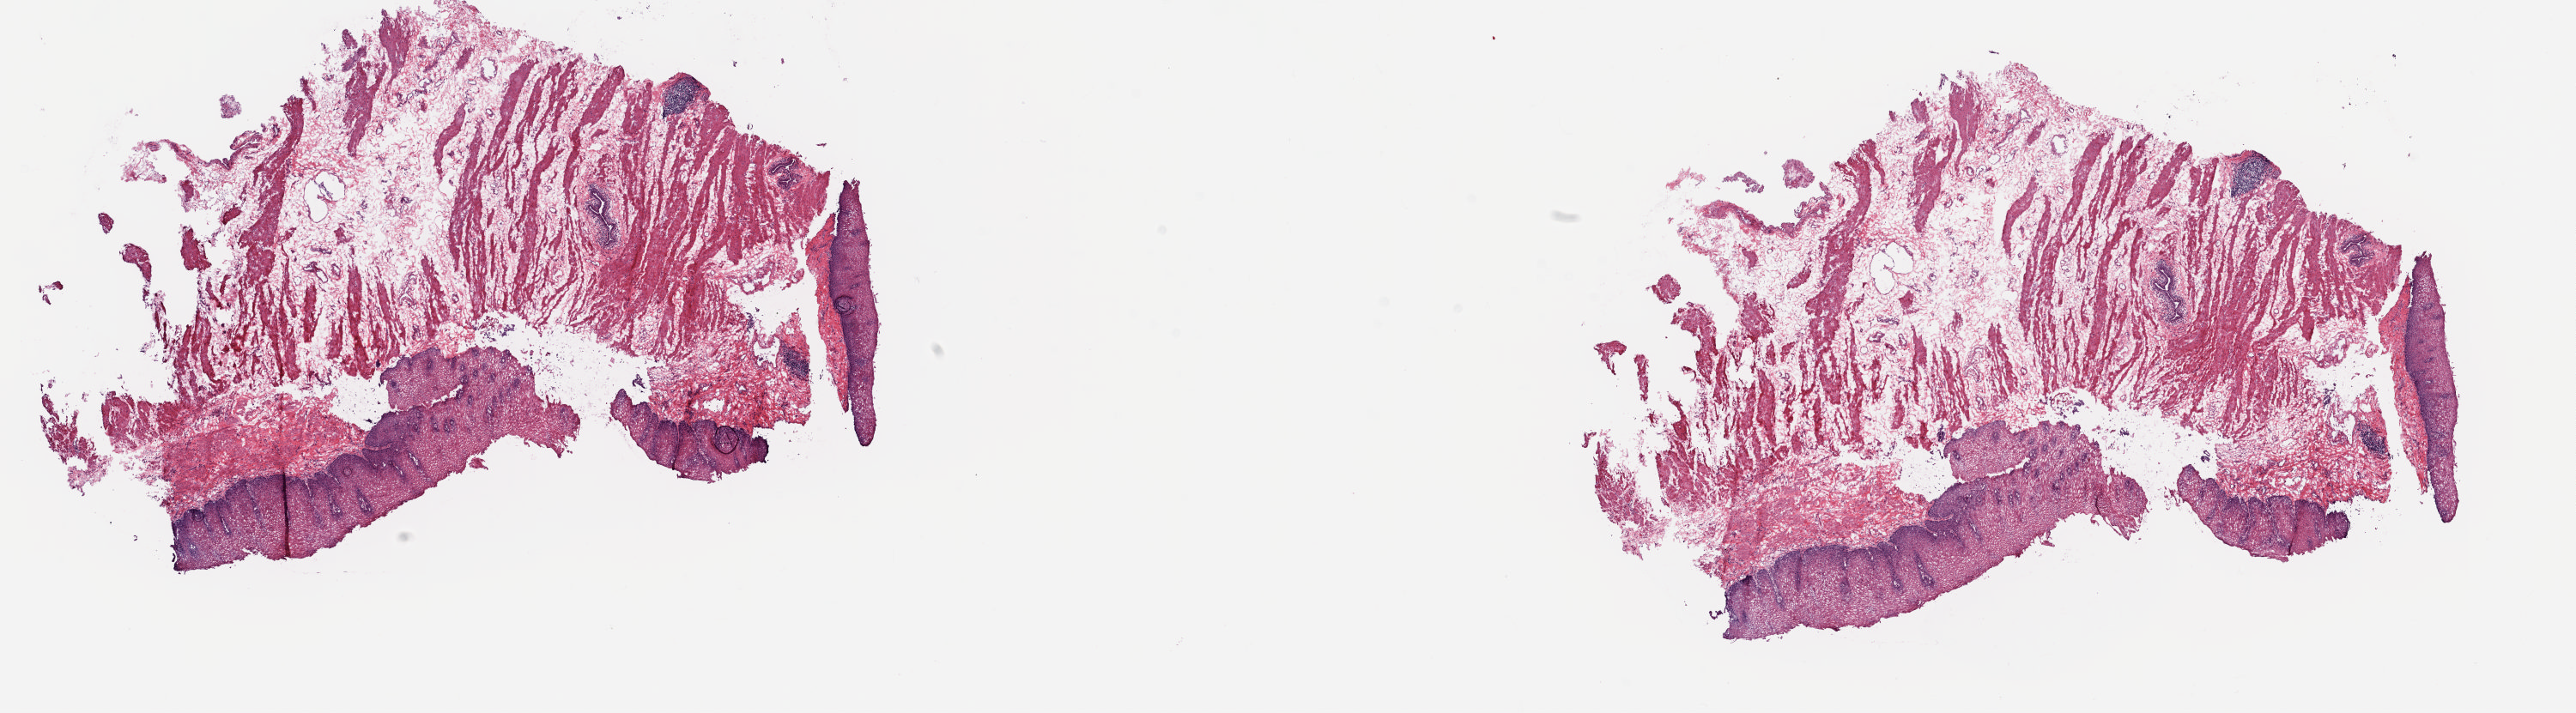
Digitized Hematoxylin and eosin (H&E) stained tissue section (whole slide), low-resolution overview of the scanned area, about 23.8 x 6.6 mm. Frozen section. Sample: solid tissue normal (non-tumour tissue), esophagus. Patient: male, age at initial diagnosis 59 years. Slide review estimates, as recorded: tumour cells 0%, tumour nuclei 0%, normal cells 15%, stromal cells 85%, necrosis 0%. Infiltration values recorded for this section: lymphocyte infiltration 5%, monocyte infiltration 0%, neutrophil infiltration 0%.
- this section: solid tissue normal (non-tumour) sample from the same patient
- patient diagnosis: Adenocarcinoma, NOS (lower third of esophagus)